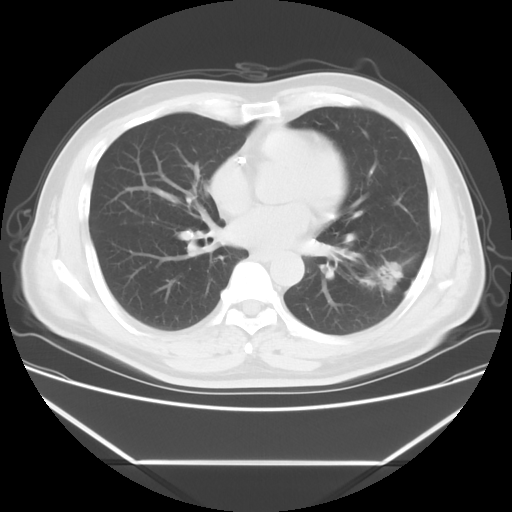
Chest CT, one axial slice; position 27 of 57 along the scan axis; reconstruction kernel STANDARD; lung window (W 1500 / L -600 HU); 5 mm slice thickness; 512 × 512 image matrix, field of view 384 × 384 mm. Patient: male, 53 years. Case-level facts recorded for this patient, not image findings: clinical TNM (as recorded): T1c N0 M0.
Outlined on this slice (bounding box drawn by a radiologist):
- lung tumour (recorded histology: adenocarcinoma): bounding box <362,253,407,306> (left, top, right, bottom; pixels)